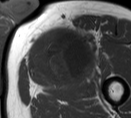
MRI of an extremity soft-tissue mass, one axial slice; position 48 of 55 along the scan axis; MR volume resampled by the dataset authors to the PET/CT grid (not the native acquisition matrix); 3.27 mm slice thickness; 131 × 118 image matrix. Male patient. Case-level facts recorded for this patient, not image findings: histological type: pleiomorphic liposarcoma; grade: high; site of the primary tumour: left thigh.
Structures marked on this image (expert contour drawn on MRI and transferred to this co-registered scan by the dataset authors):
- gross tumour volume including surrounding oedema: bounding box [x1, y1, x2, y2] px = [30, 25, 97, 79]
- gross tumour volume (mass): [30, 32, 85, 78]